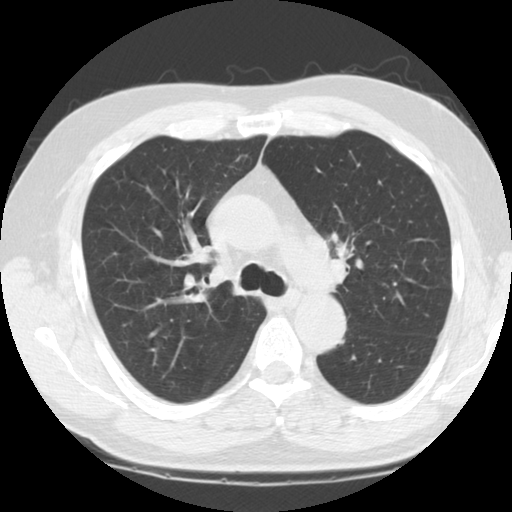
Chest CT (low-dose screening protocol), one axial image, third annual screen, lung window (W 1500 / L -600 HU), 2.5 mm slice thickness. Male, age 60 years at enrolment. Current smoker at enrolment.
• Expert reader's lesion annotation, bounding box <314,219,369,271> (left, top, right, bottom; pixels).
• Reader record for this screening exam (exam-level; its link to the box is not recorded): non-calcified nodule or mass ≥4 mm, left upper lobe, 24 × 21 mm, smooth margins, soft tissue attenuation, pre-existing on the prior screen: no.
• Official screen result: positive, other.
• Participant outcome: lung cancer diagnosed 14 days after this screen — small cell carcinoma, NOS, left upper lobe, stage IIA (AJCC 6th edition), 26 mm at pathology.